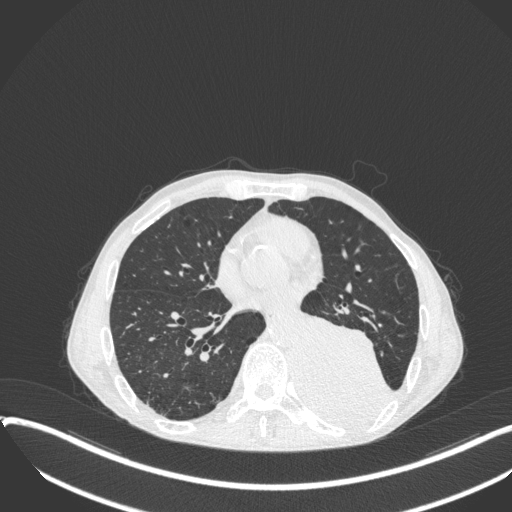
Chest CT, one axial slice; position 155 of 400 along the scan axis; reconstruction kernel B31f; lung window (W 1500 / L -600 HU); 1 mm slice thickness; 512 × 512 image matrix, field of view 400 × 400 mm. Male patient, age 57 years. Case-level facts recorded for this patient, not image findings: clinical TNM (as recorded): T4 N0 M0.
Outlined on this slice (rectangle marked by the reading radiologist):
- lung tumour (recorded histology: squamous cell carcinoma): box from (x=295, y=308) to (x=395, y=429) px